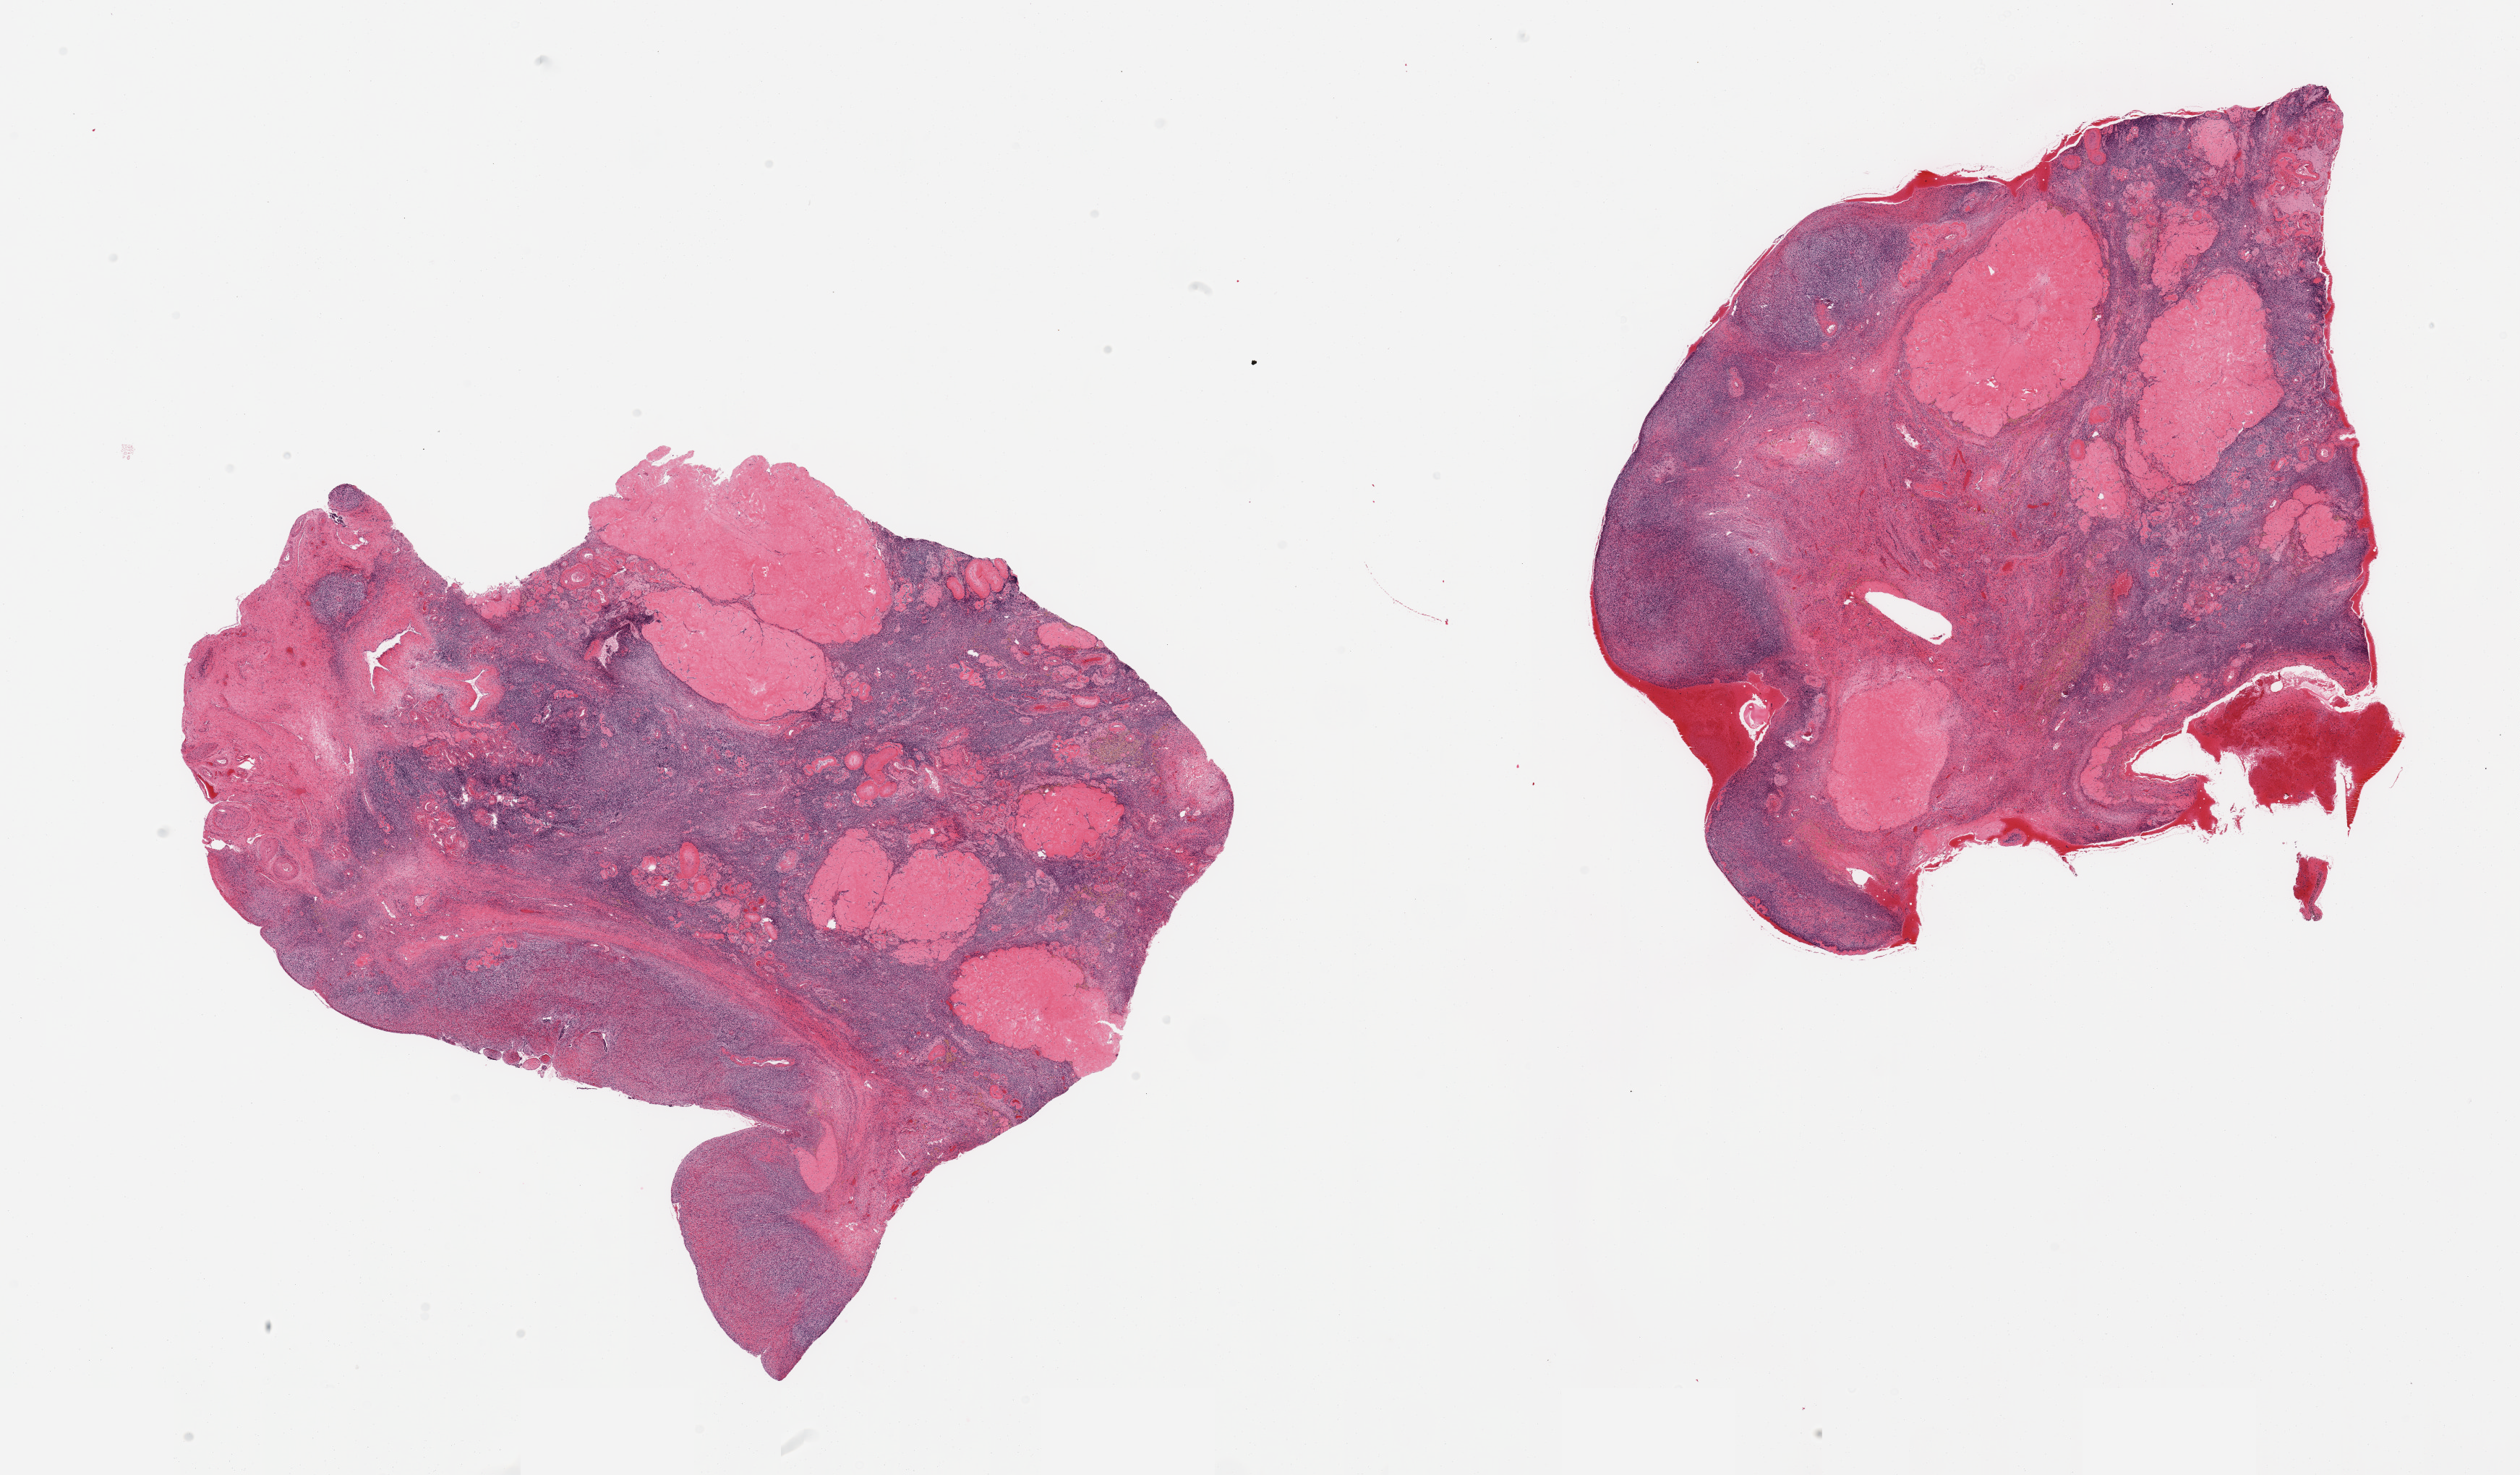
Digitized H&E-stained section — whole scanned area (about 27.6 x 16.1 mm) shown as a low-resolution overview. PAXgene-fixed, paraffin-embedded tissue. Sampled site (target tissue): ovary. Tissue donor sample. Donor: female.
• reviewer comment on this tissue sample: 2 pieces, no abnormalities